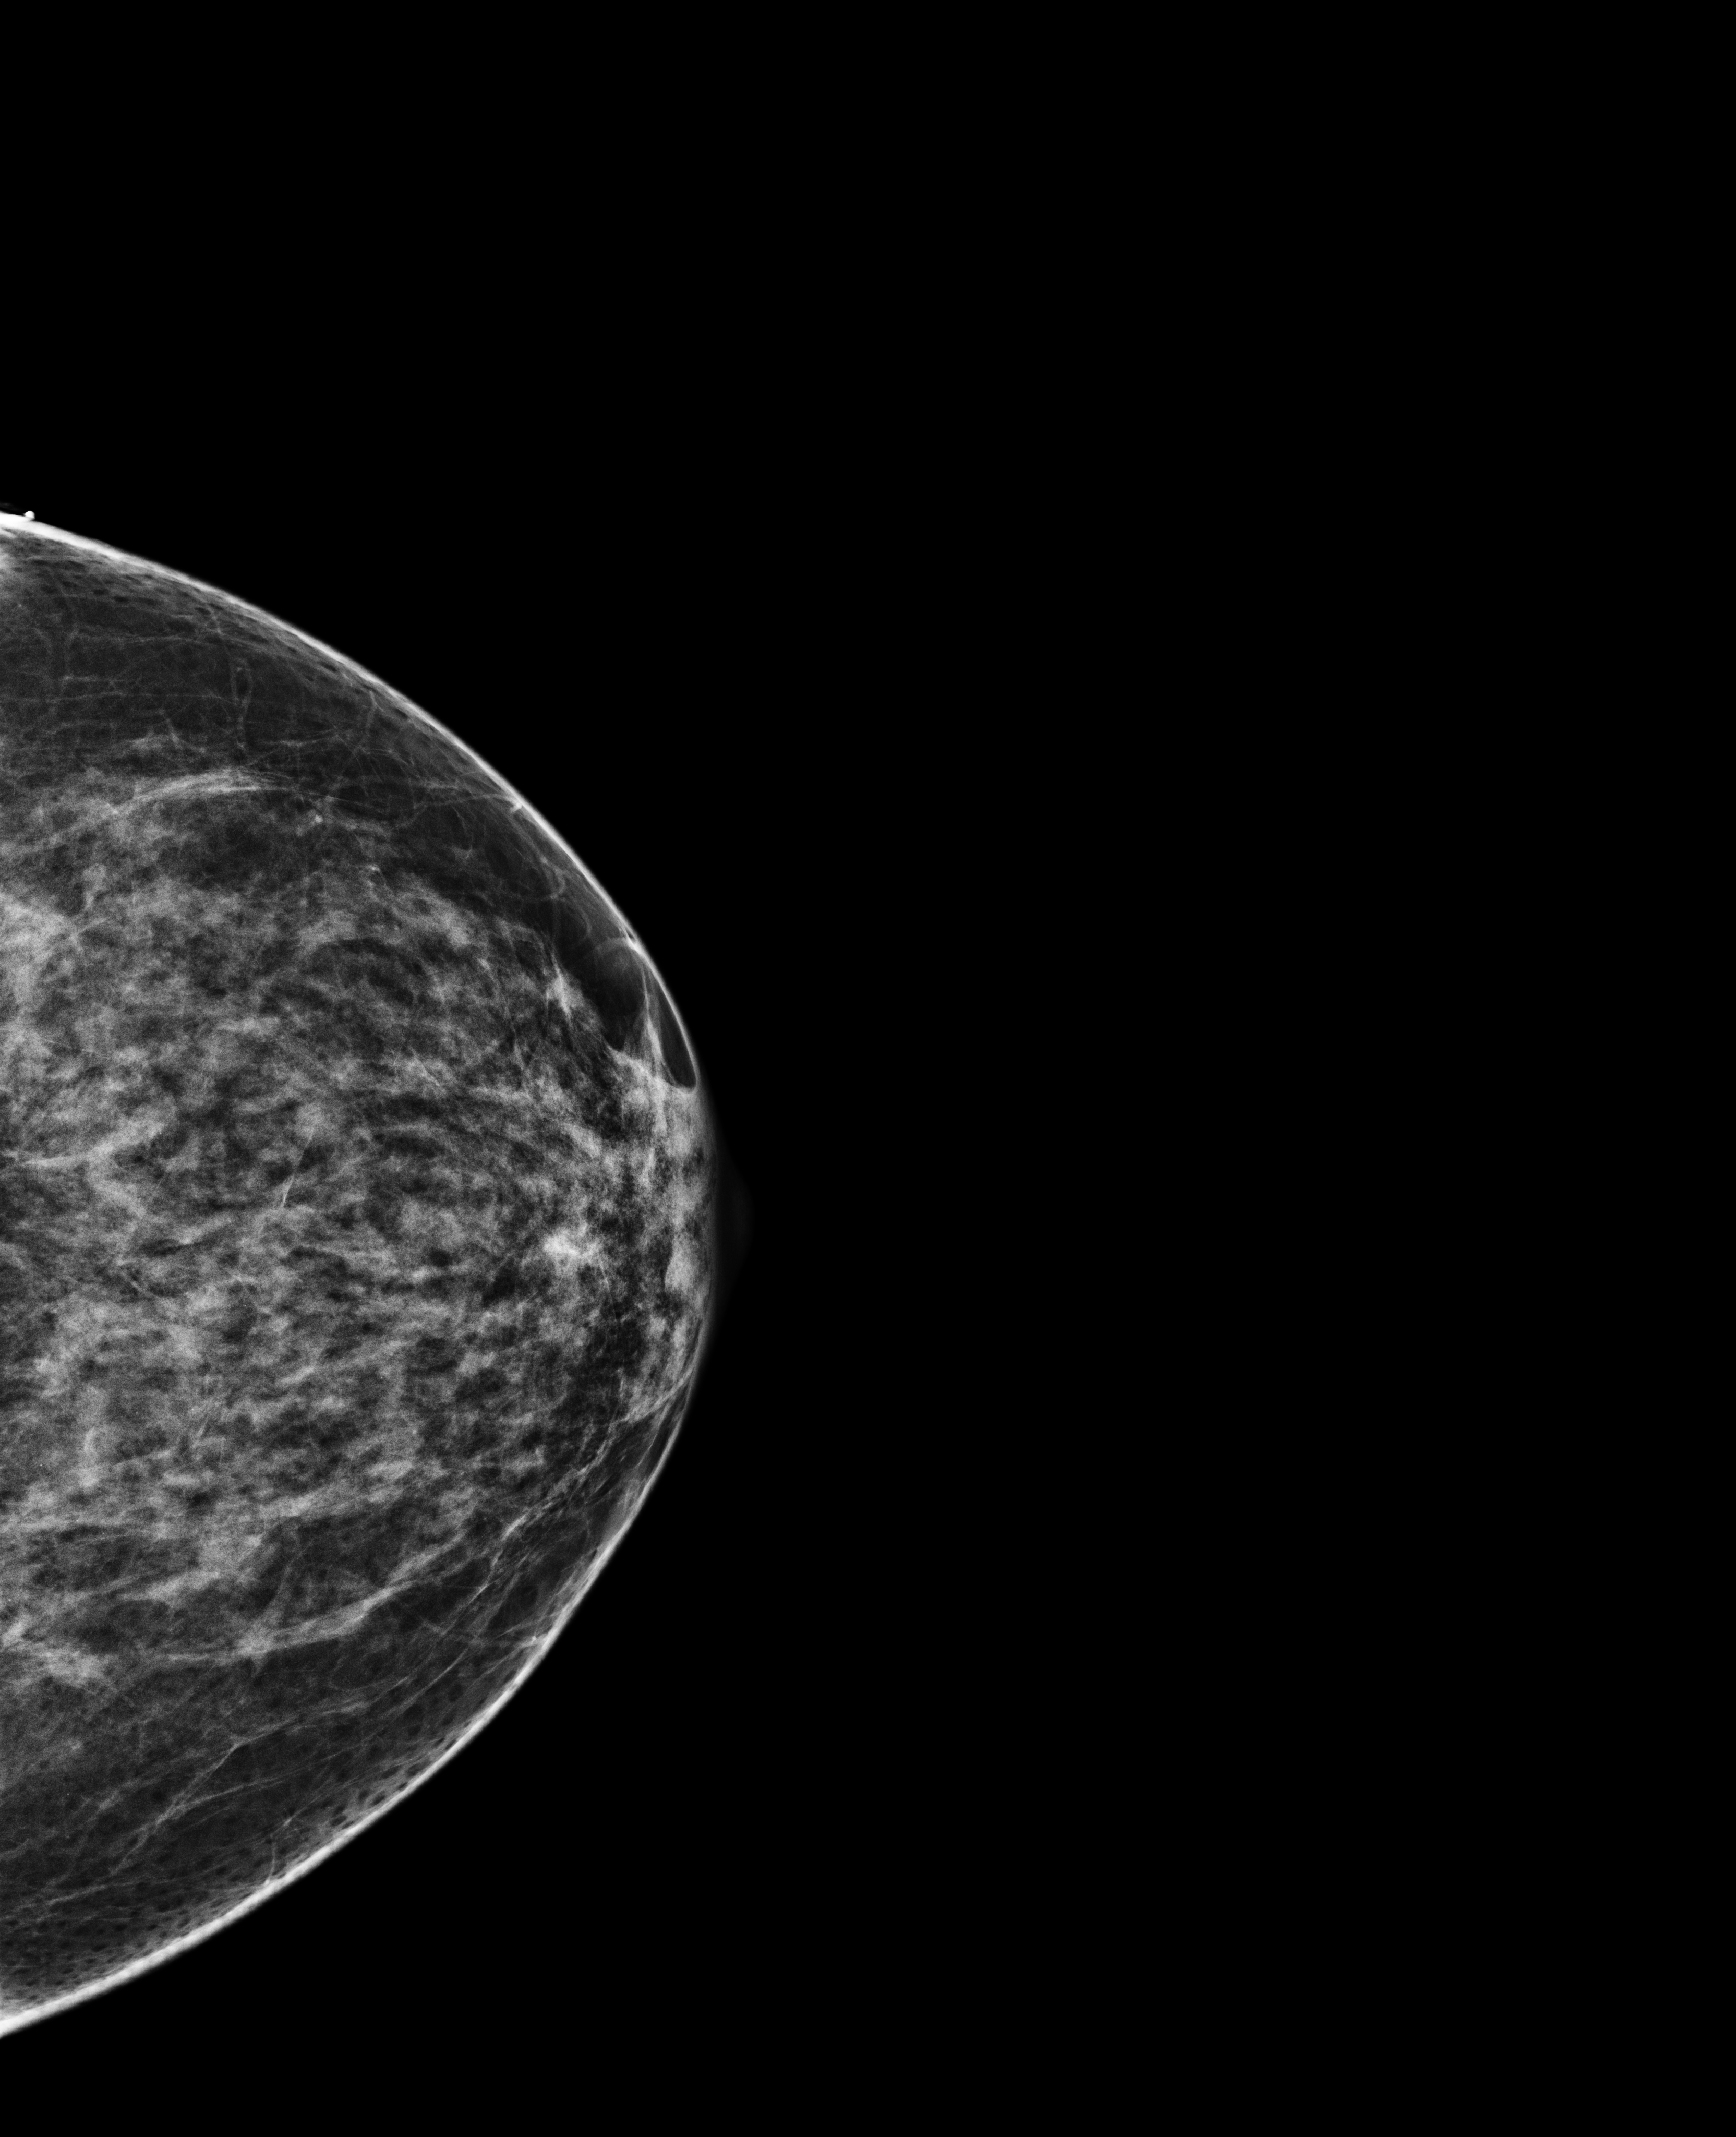
Screening examination, compressed breast thickness 67 mm. Female patient, age 53 years.
Image type: full-field digital mammogram. Breast: left. Projection: cranio-caudal projection.